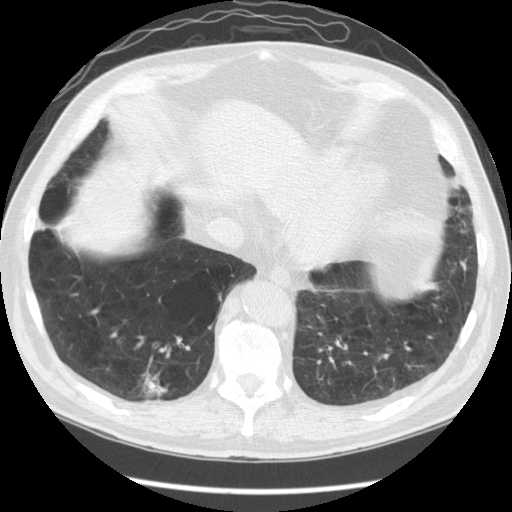
Axial slice from a low-dose chest CT screening exam; baseline annual screen; lung window (W 1500 / L -600 HU); 2.5 mm slice thickness; standard (soft-tissue) reconstruction kernel (STANDARD). Male, age 67 years at enrolment. Former smoker at enrolment.
Lesion marked by an expert reader, bounding box [x1, y1, x2, y2] px = [121, 356, 184, 412]. The screening reader recorded 2 non-calcified nodules or masses ≥4 mm on this exam (right lower lobe, right lower lobe); which of them this box marks is not recorded. Official screen result: positive, change unspecified: nodule(s) >= 4 mm or enlarging nodule(s), mass(es), or other non-specific abnormalities suspicious for lung cancer. Lung cancer was diagnosed 78 days after this screen: squamous cell carcinoma, NOS, right lower lobe, moderately differentiated (G2), stage IA (AJCC 6th edition), 23 mm at pathology.